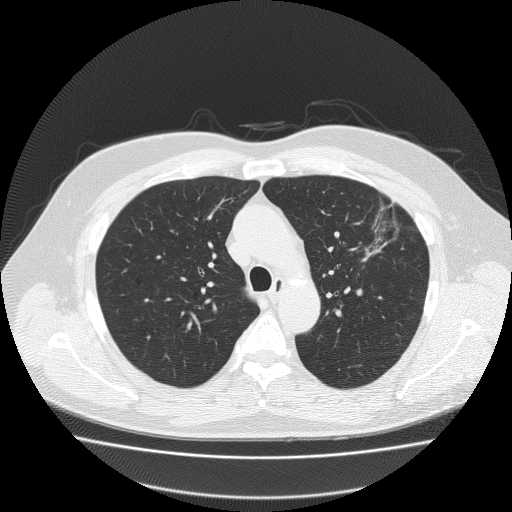
Axial slice from a low-dose chest CT screening exam; first (baseline) screen; lung window (W 1500 / L -600 HU); 2 mm slice thickness; lung (sharp) reconstruction kernel (FC51). Male participant, aged 62 years at enrolment. Former smoker at enrolment.
Lesion marked by an expert reader, bounding box [x1, y1, x2, y2] px = [358, 195, 426, 258]. The exam's reader record, not a measurement of the box and not confirmed to be the same lesion: non-calcified nodule or mass ≥4 mm, left upper lobe, 18 × 8 mm, spiculated (stellate) margins, soft tissue attenuation. Official screen result: positive, change unspecified: nodule(s) >= 4 mm or enlarging nodule(s), mass(es), or other non-specific abnormalities suspicious for lung cancer.